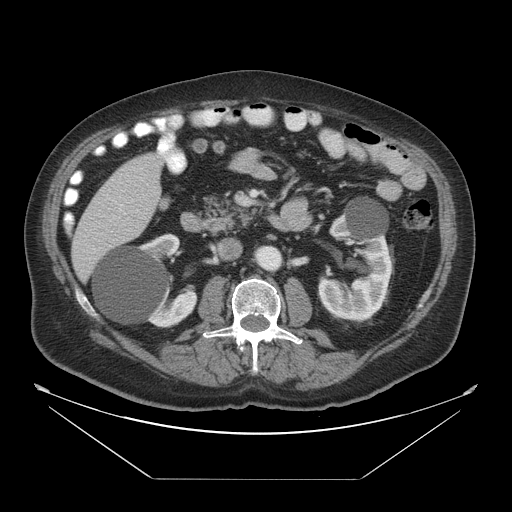
Contrast-enhanced abdominal CT, one axial slice; slice 17 of 45 in the series (ordered by position); 120 kVp; intravenous contrast given; soft-tissue window (W 400 / L 40 HU); 5 mm slice thickness; 512 × 512 image matrix, field of view 463 × 463 mm. Male patient, age 87 years. Case-level facts recorded for this patient, not image findings: diagnosis: colorectal cancer liver metastases, imaged before liver resection; multiple liver metastases: no; largest metastasis: 4.5 cm; disease in both lobes: yes.
Structures marked on this image (manually delineated by an expert):
- liver: bounding box [x1, y1, x2, y2] px = [71, 154, 164, 283]
- portal vein (with intrahepatic branches): [124, 213, 129, 219]